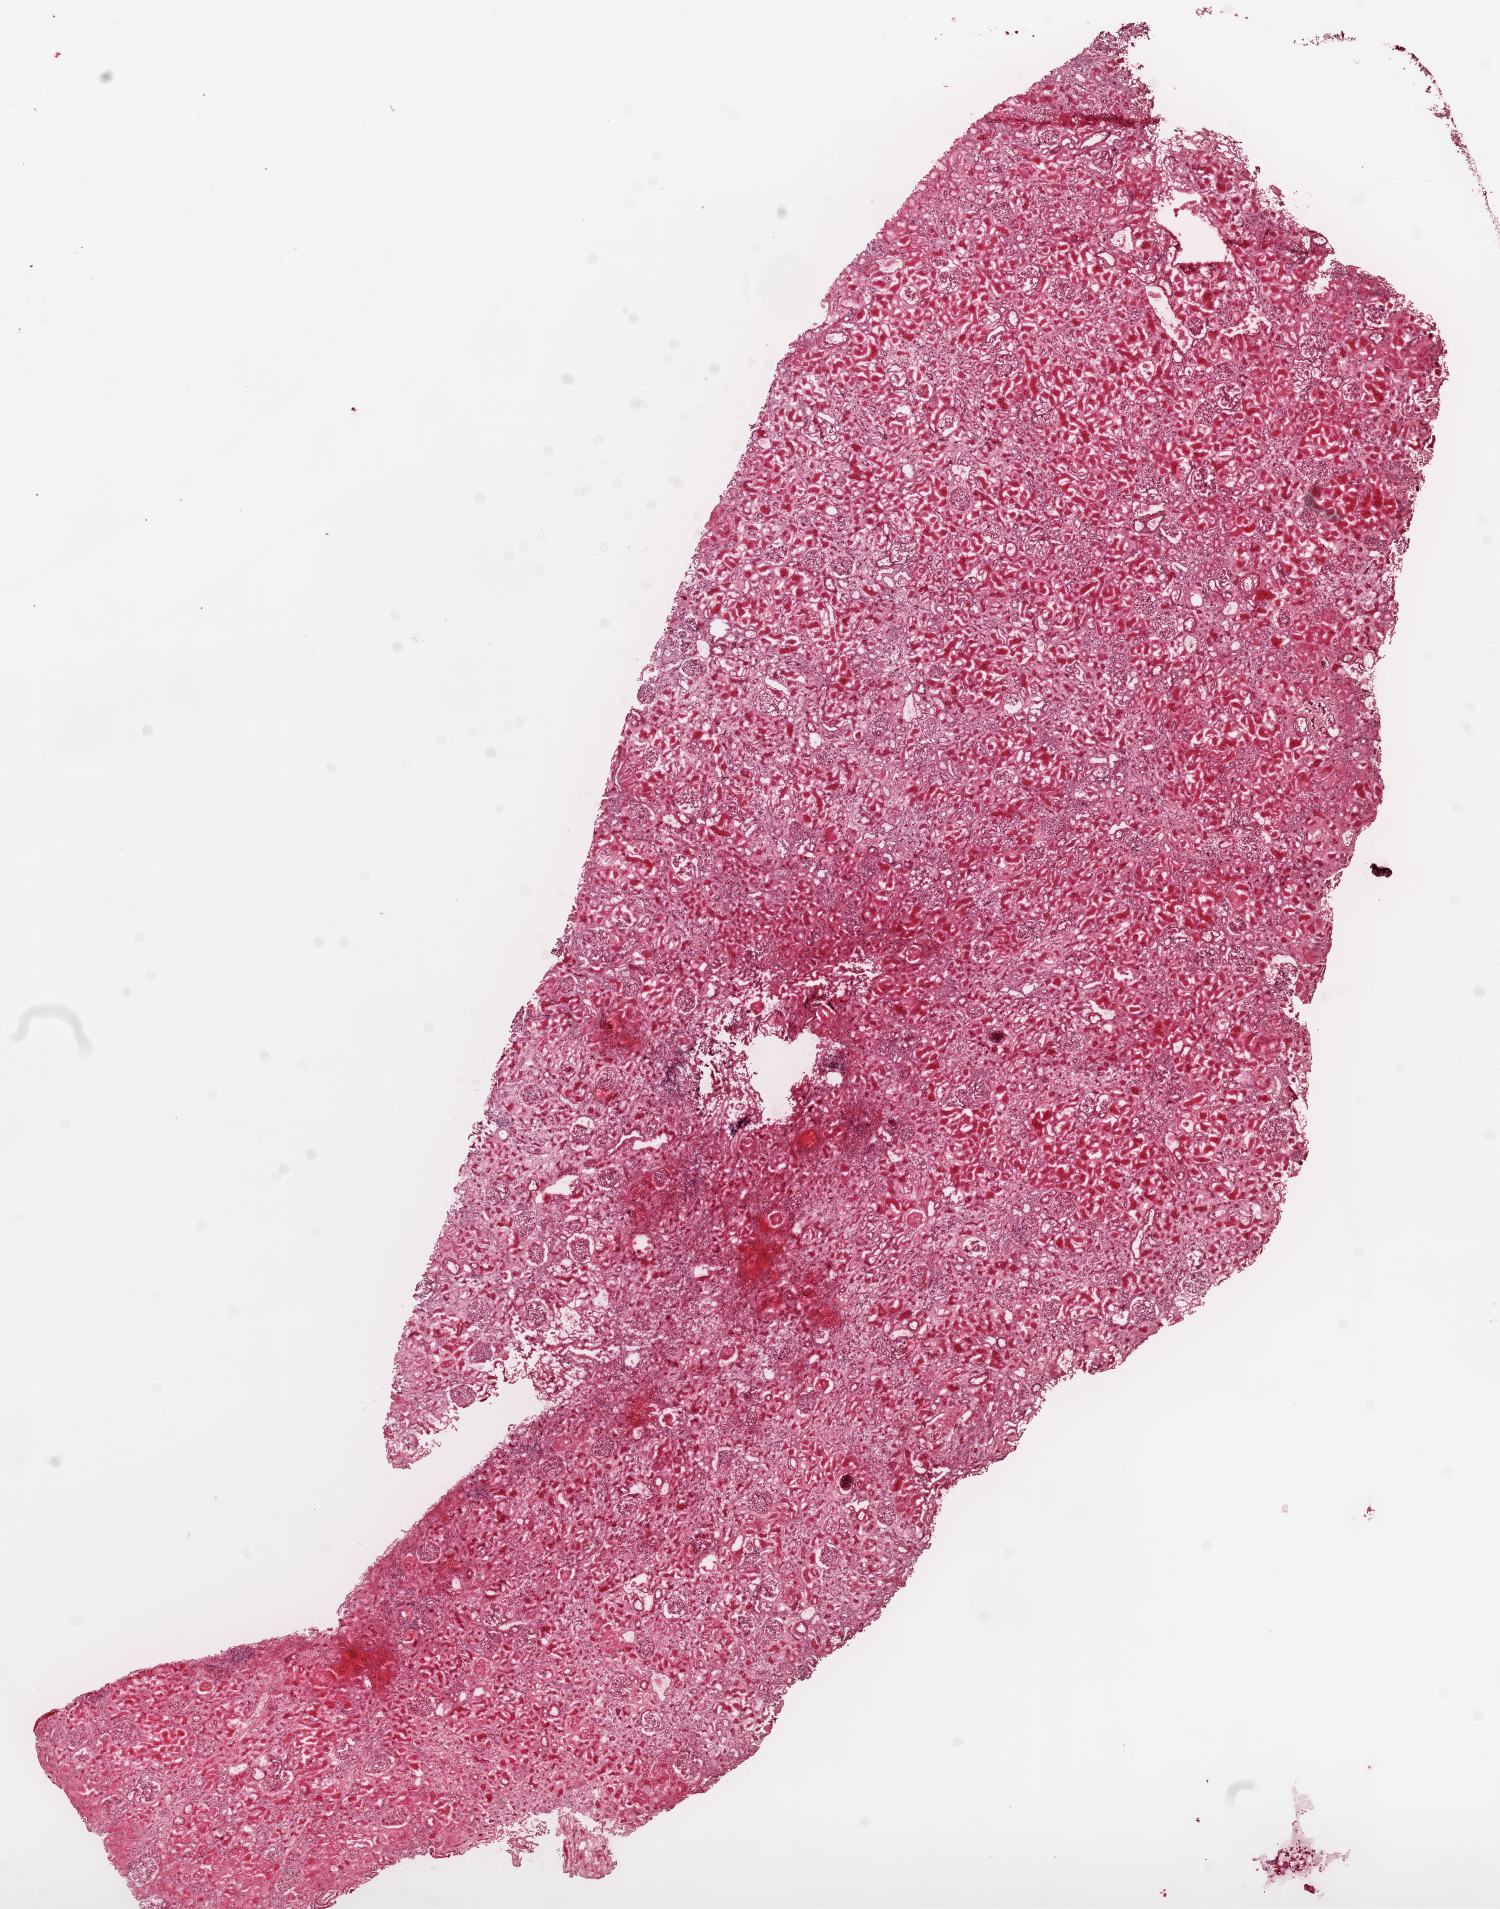
Digitized Hematoxylin and eosin (H&E) stained tissue section (whole slide) — shown as a low-resolution overview of the whole scanned area (about 12.0 x 15.3 mm). Frozen section. Sample: solid tissue normal (non-tumour tissue), kidney. Male, age 78 years at initial diagnosis.
- this section: solid tissue normal sample (biorepository sample class)
- patient diagnosis: Clear cell adenocarcinoma, NOS